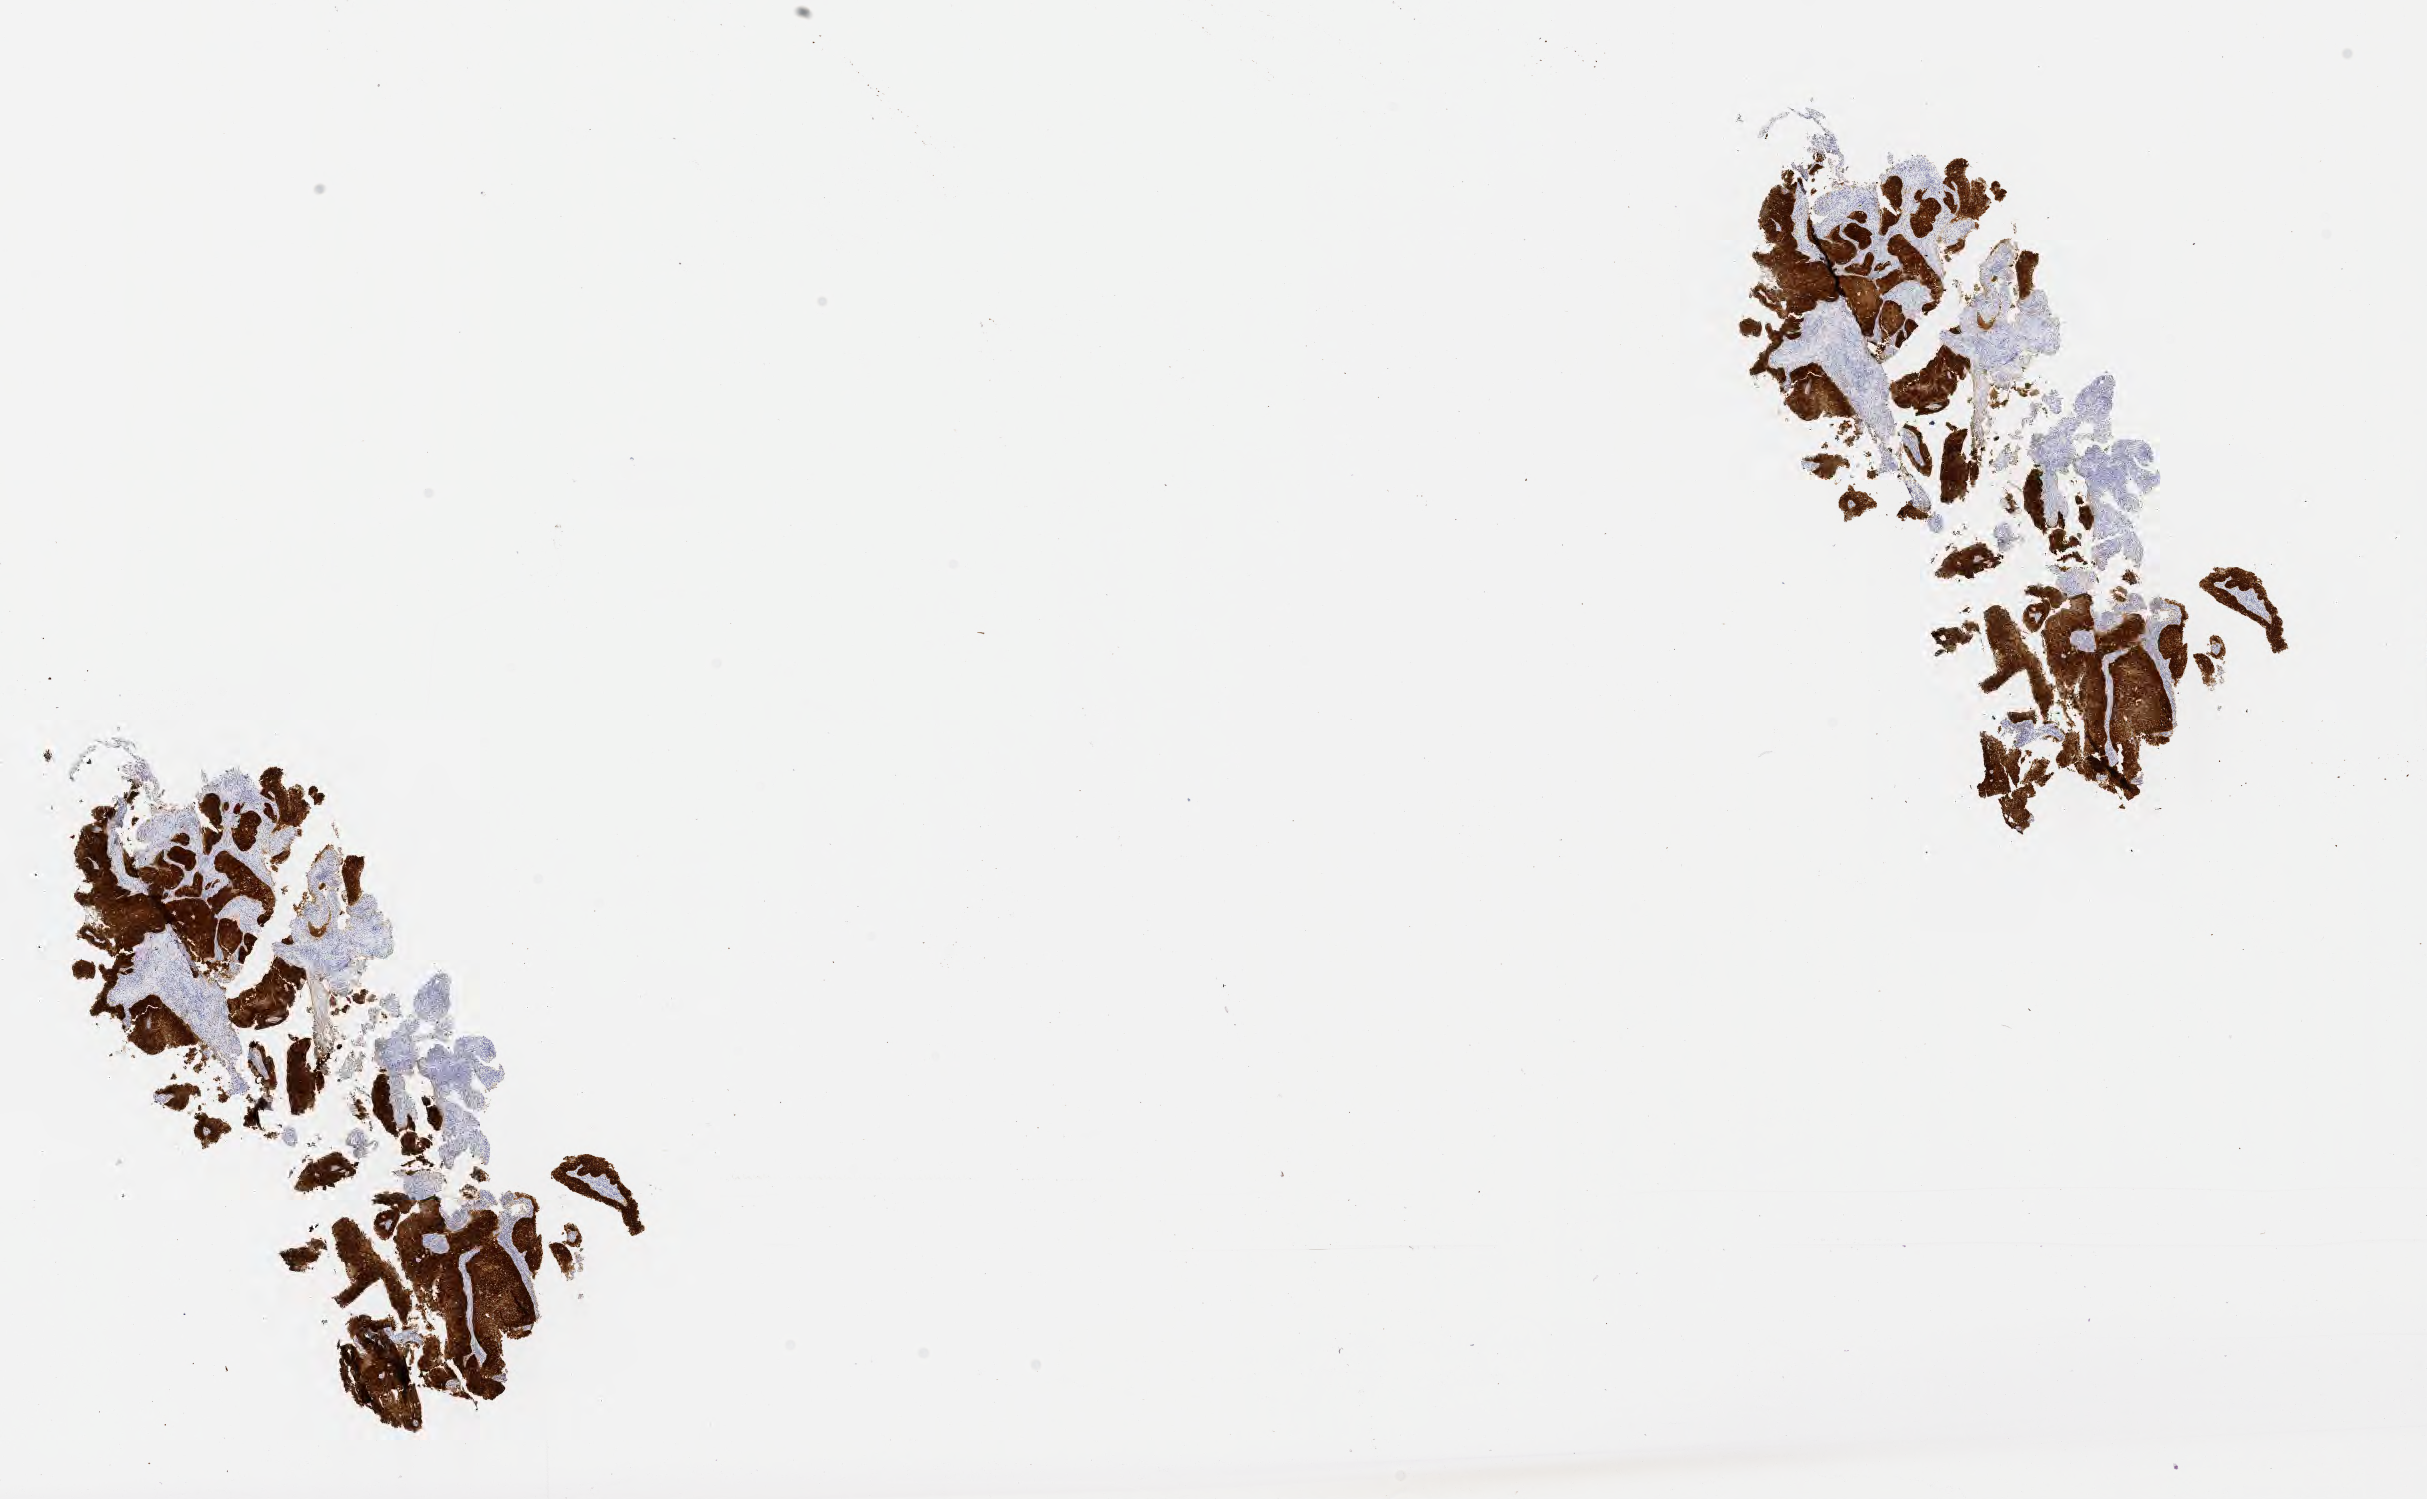
IHC for p16 (p16INK4a), whole-slide image — whole scanned area (about 19.6 x 12.1 mm) shown as a low-resolution overview, specimen: tumor tissue, anatomic site: cervix. Female patient, aged 31.
Histologic diagnosis: Squamous cell carcinoma, large cell, nonkeratinizing, NOS.